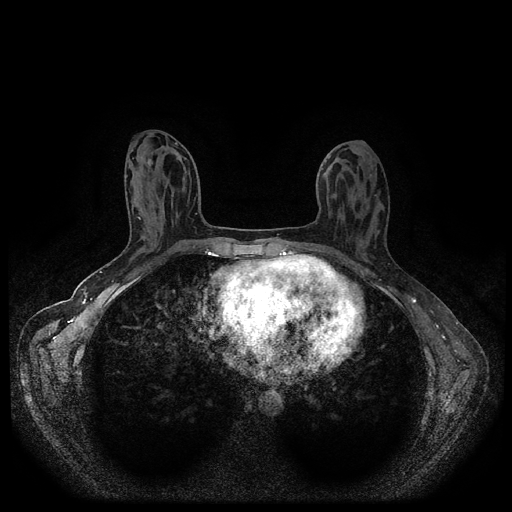
Breast MRI (dynamic contrast-enhanced, multi-phase), one axial slice. Slice 42 of 116 in the series (ordered by position). Dynamic contrast-enhanced series, time point 2 of 5 at this slice position (early post-contrast). 1.5 T. TE 2.6 ms, TR 5.4 ms. 512 × 512 image matrix, field of view 340 × 340 mm. Female patient, age 30 years.
Structures marked on this image (semi-automatic segmentation, software-assisted and operator-edited):
- breast lesion (labelled benign in the annotation): box from (x=146, y=158) to (x=155, y=168) px